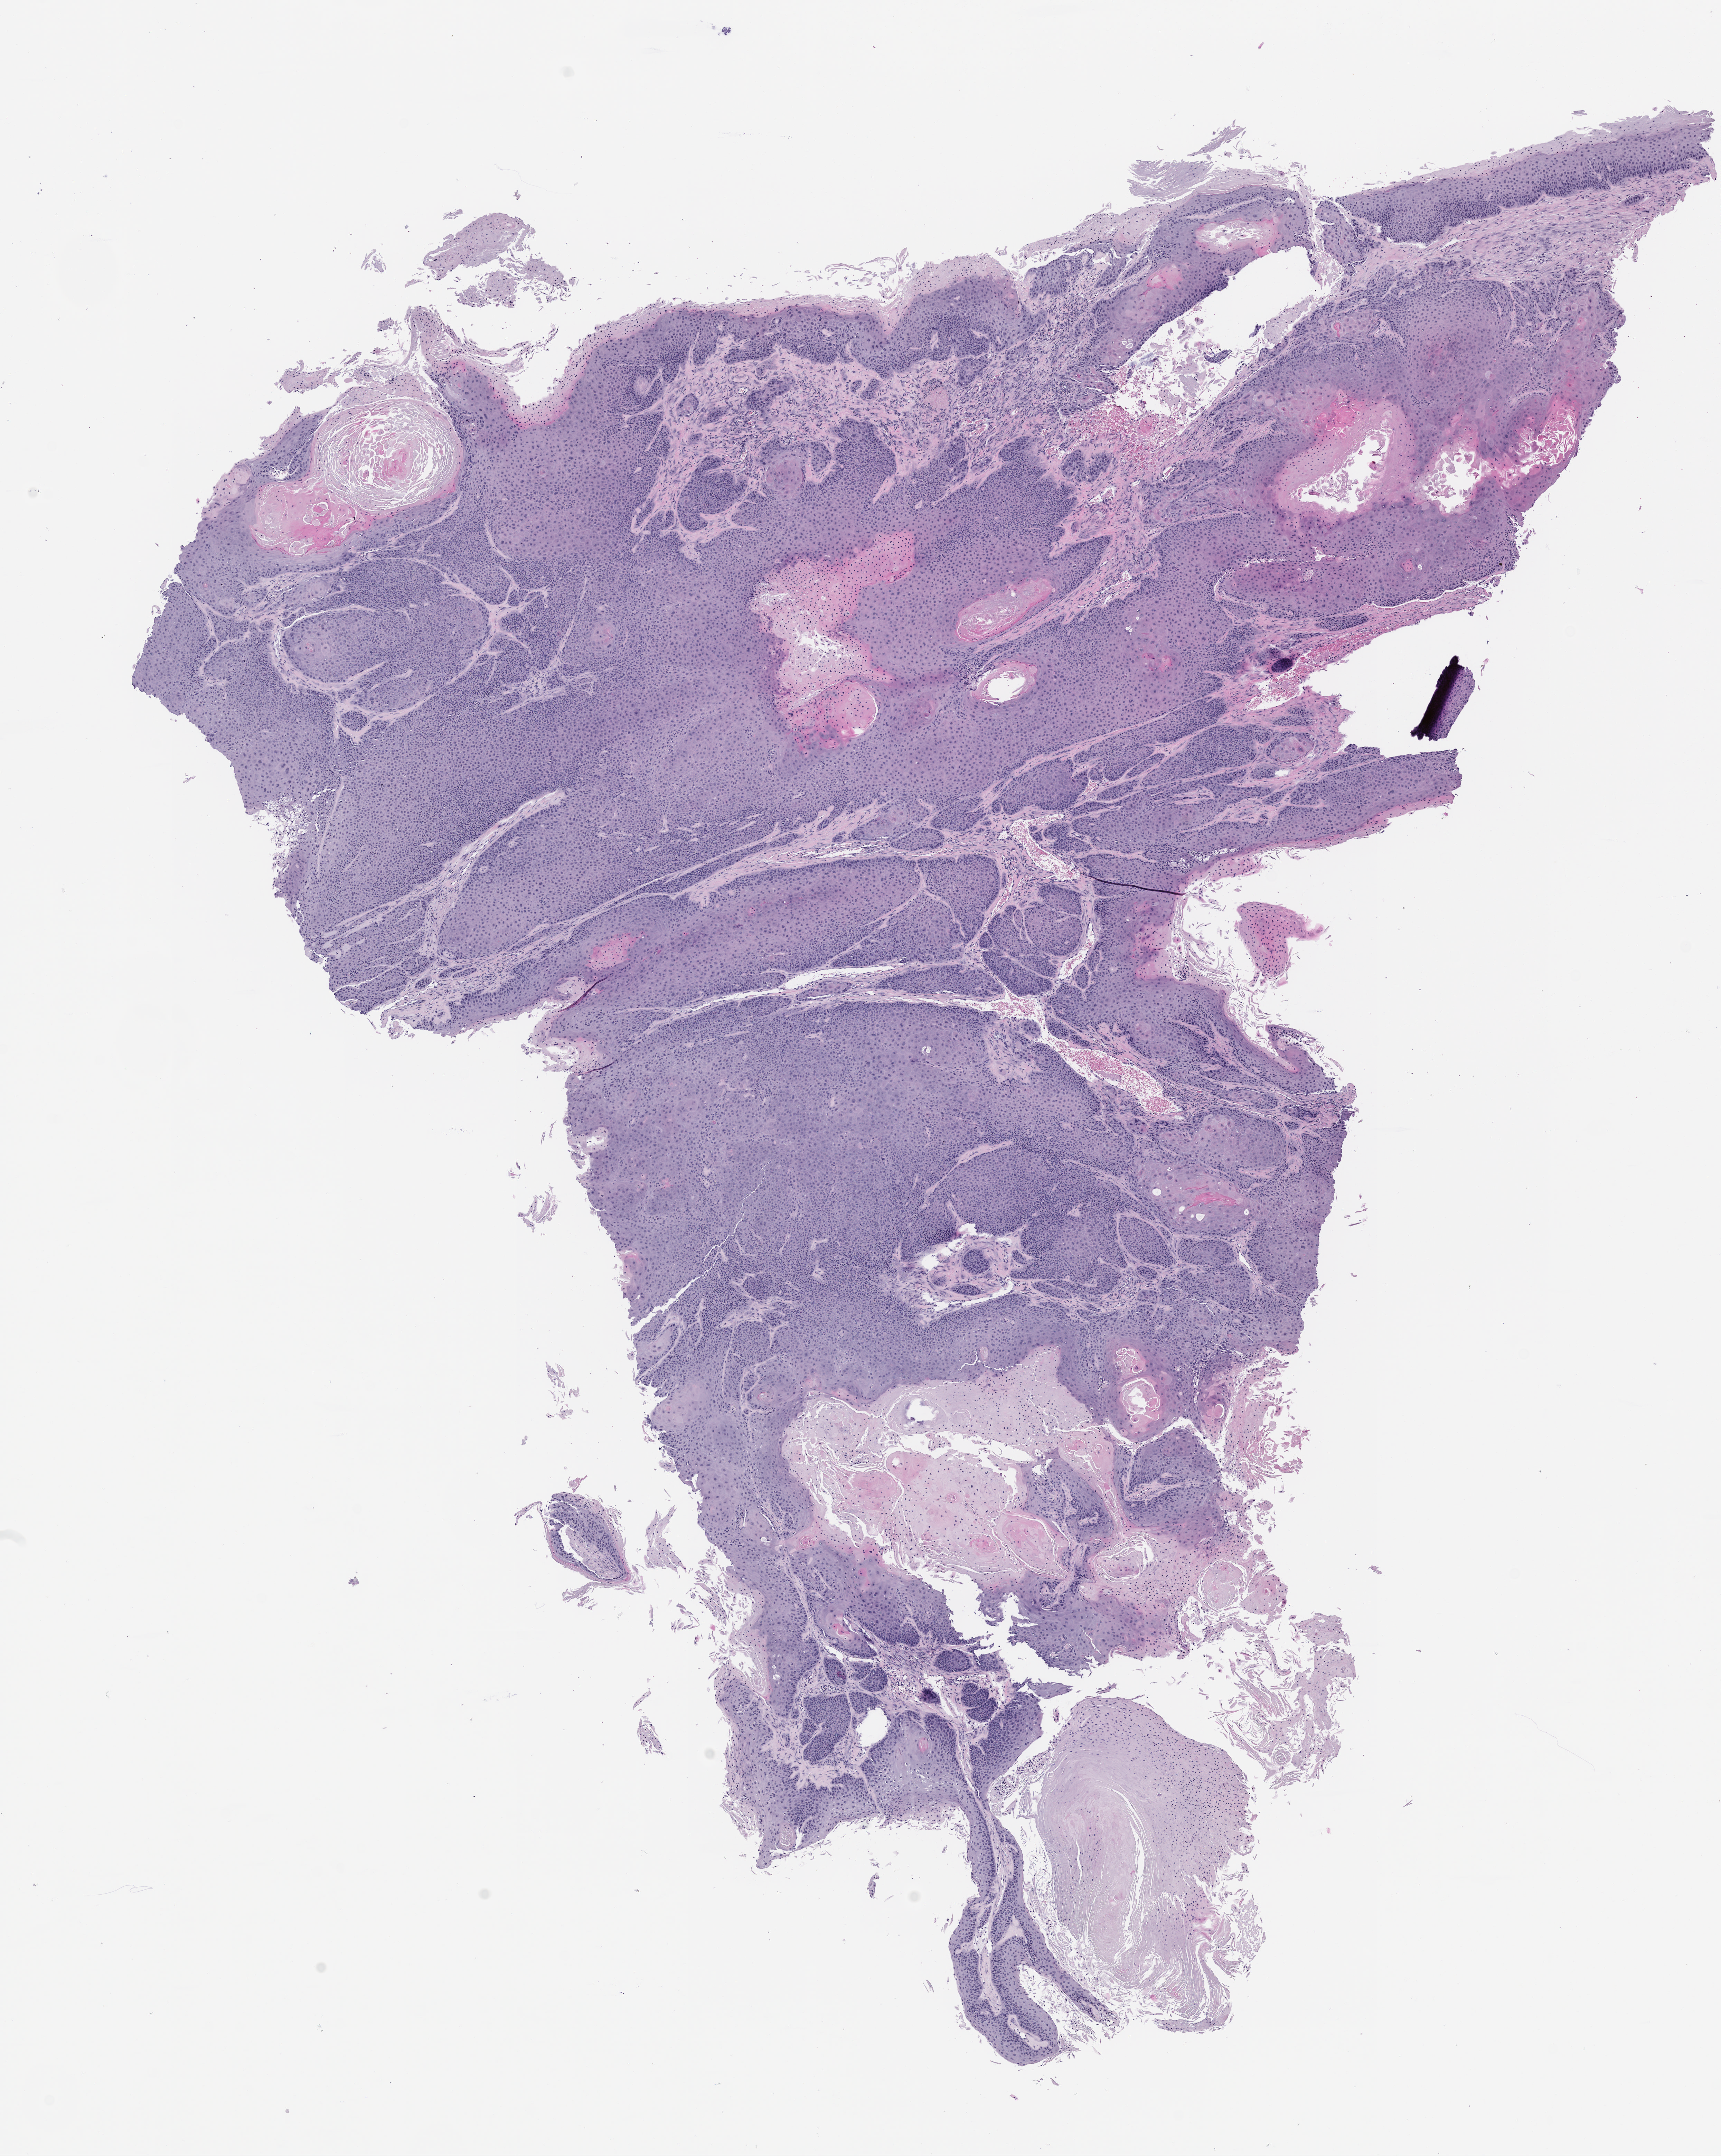
Whole-slide image, hematoxylin and eosin (H&E): patient-derived xenograft (human tumor grown in a mouse), passage 3, low-resolution overview of the scanned area, about 10.0 x 12.5 mm; formalin-fixed, paraffin-embedded (FFPE) tissue; originating tumor site category: oral soft tissue.
Originating patient diagnosis: Head and Neck Squamous Cell Carcinoma.